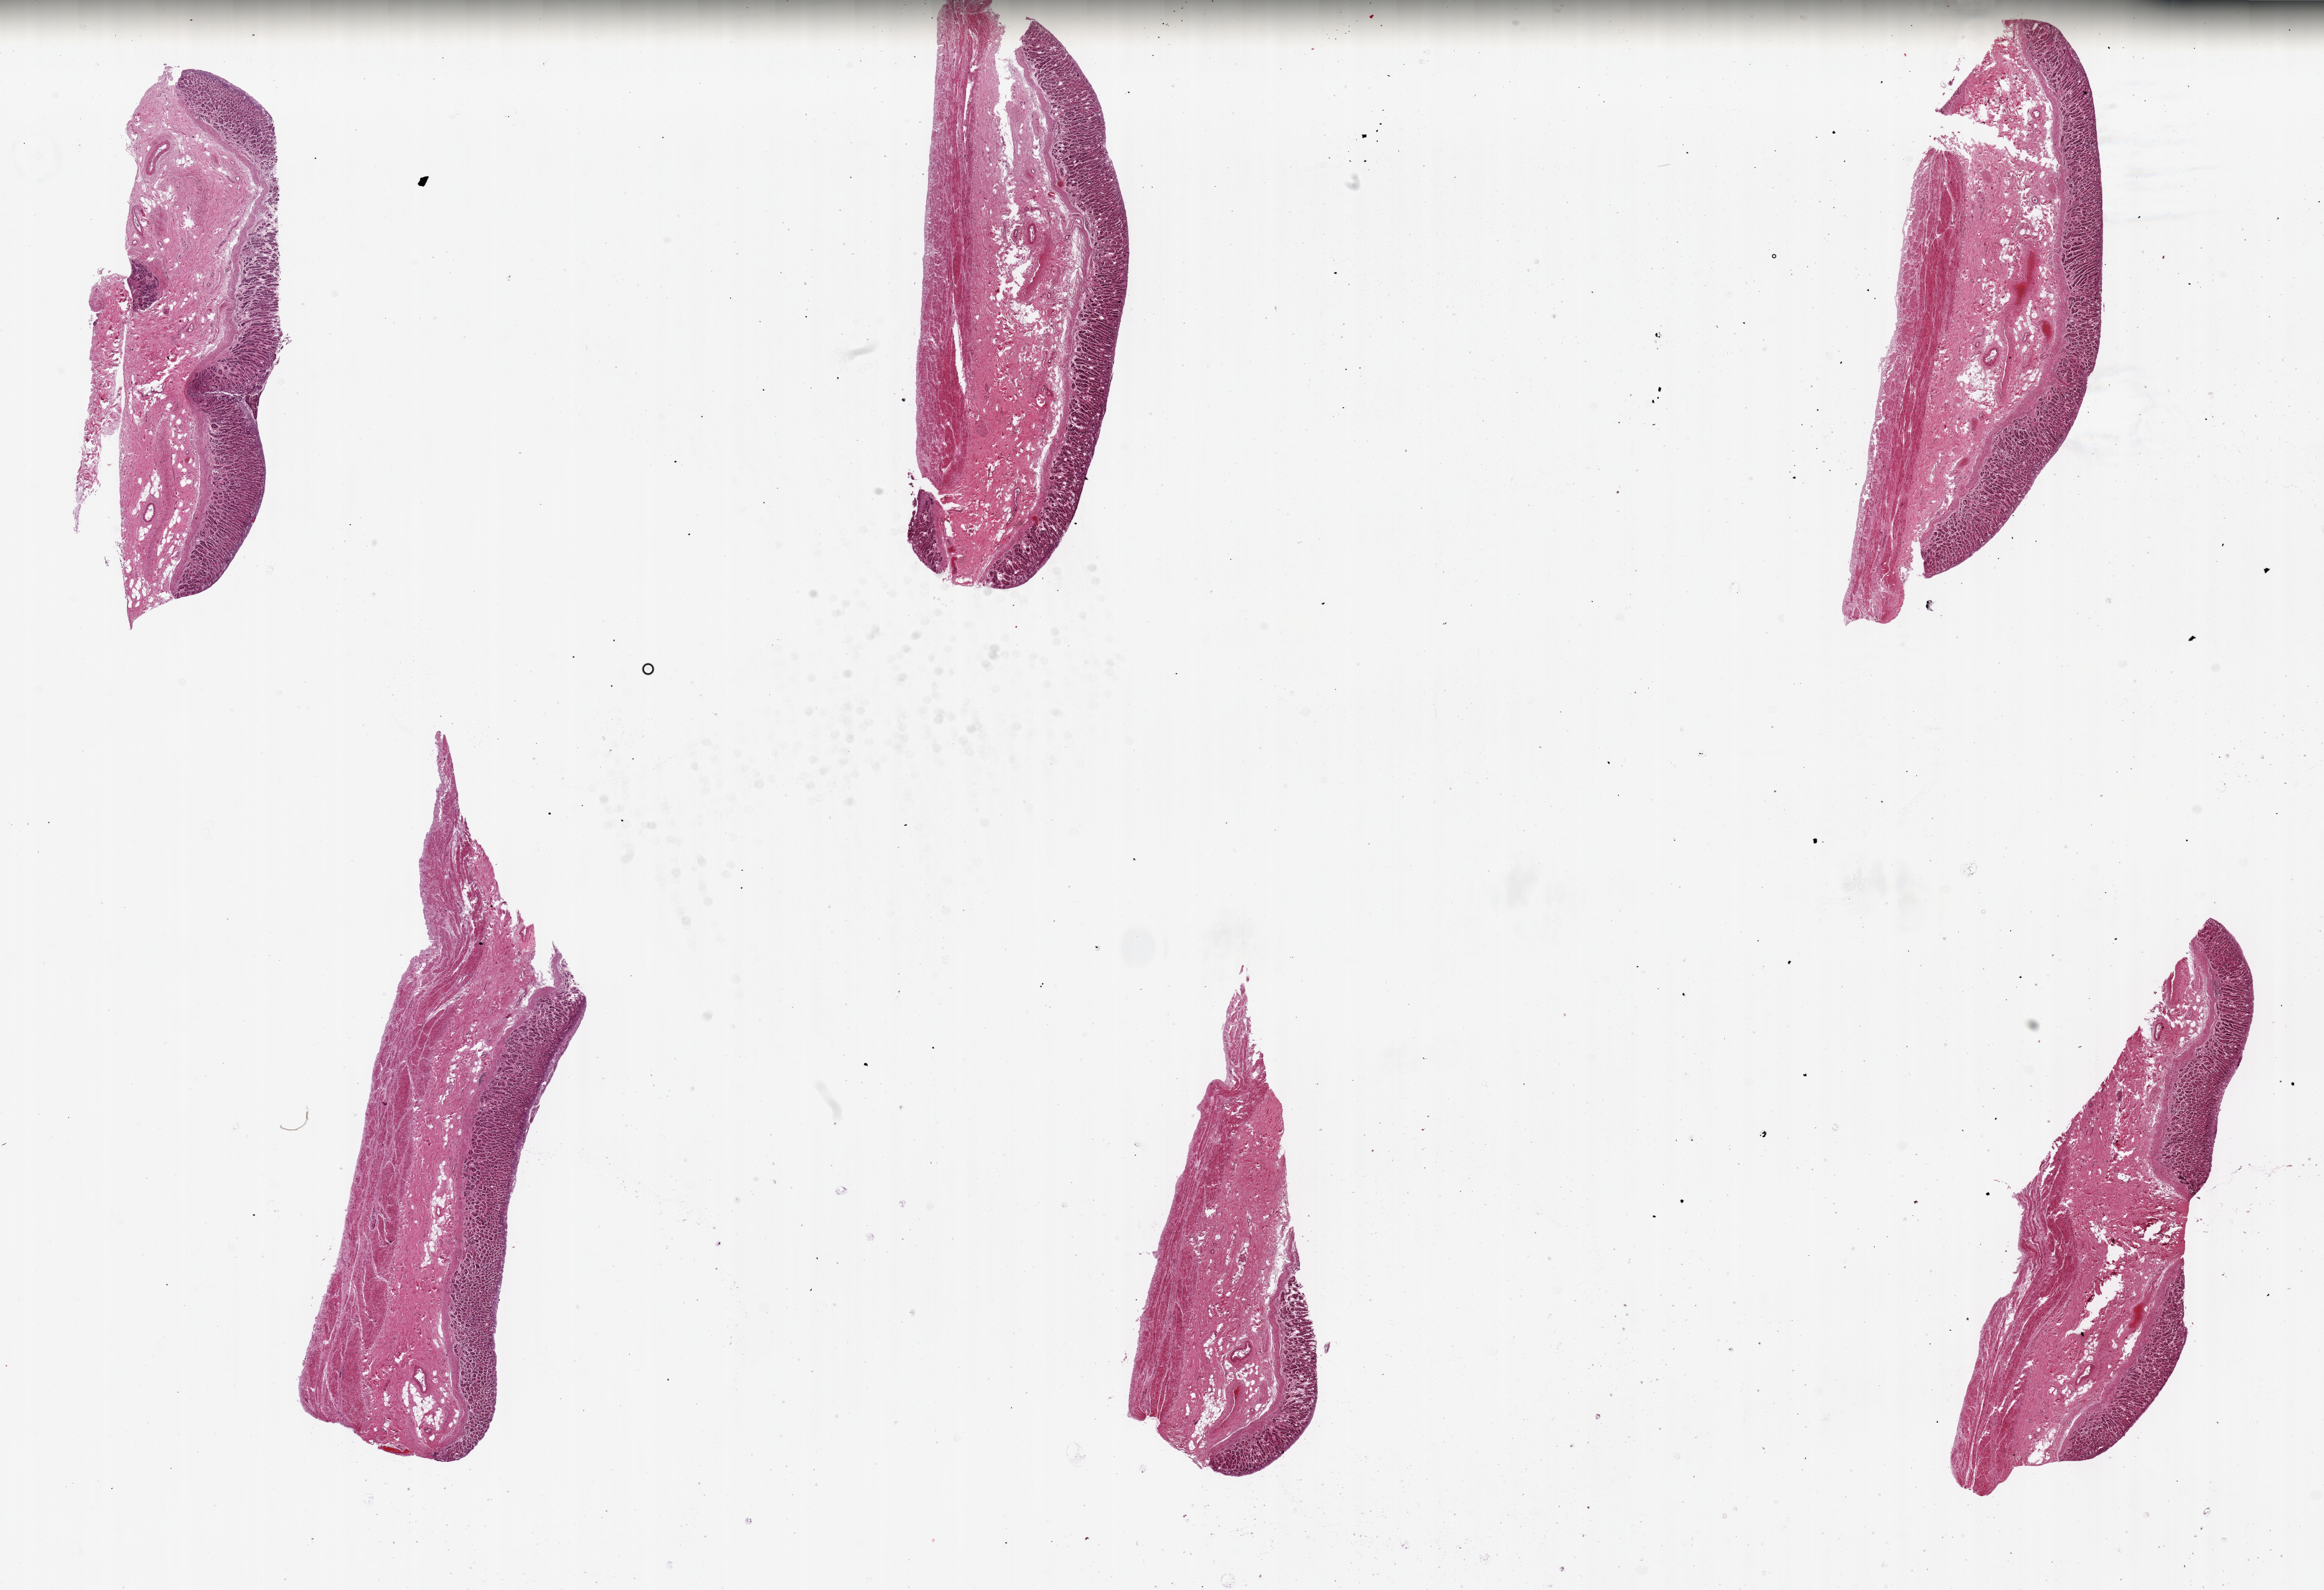
H&E whole-slide image, brightfield, a low-resolution overview of the entire scanned area, about 29.5 x 20.2 mm. PAXgene-fixed, paraffin-embedded tissue. Target tissue: stomach. Donor tissue sample. Male donor.
Review note (as recorded): 6 pieces, up to 9x2mm; mucosa moderately autolyzed.